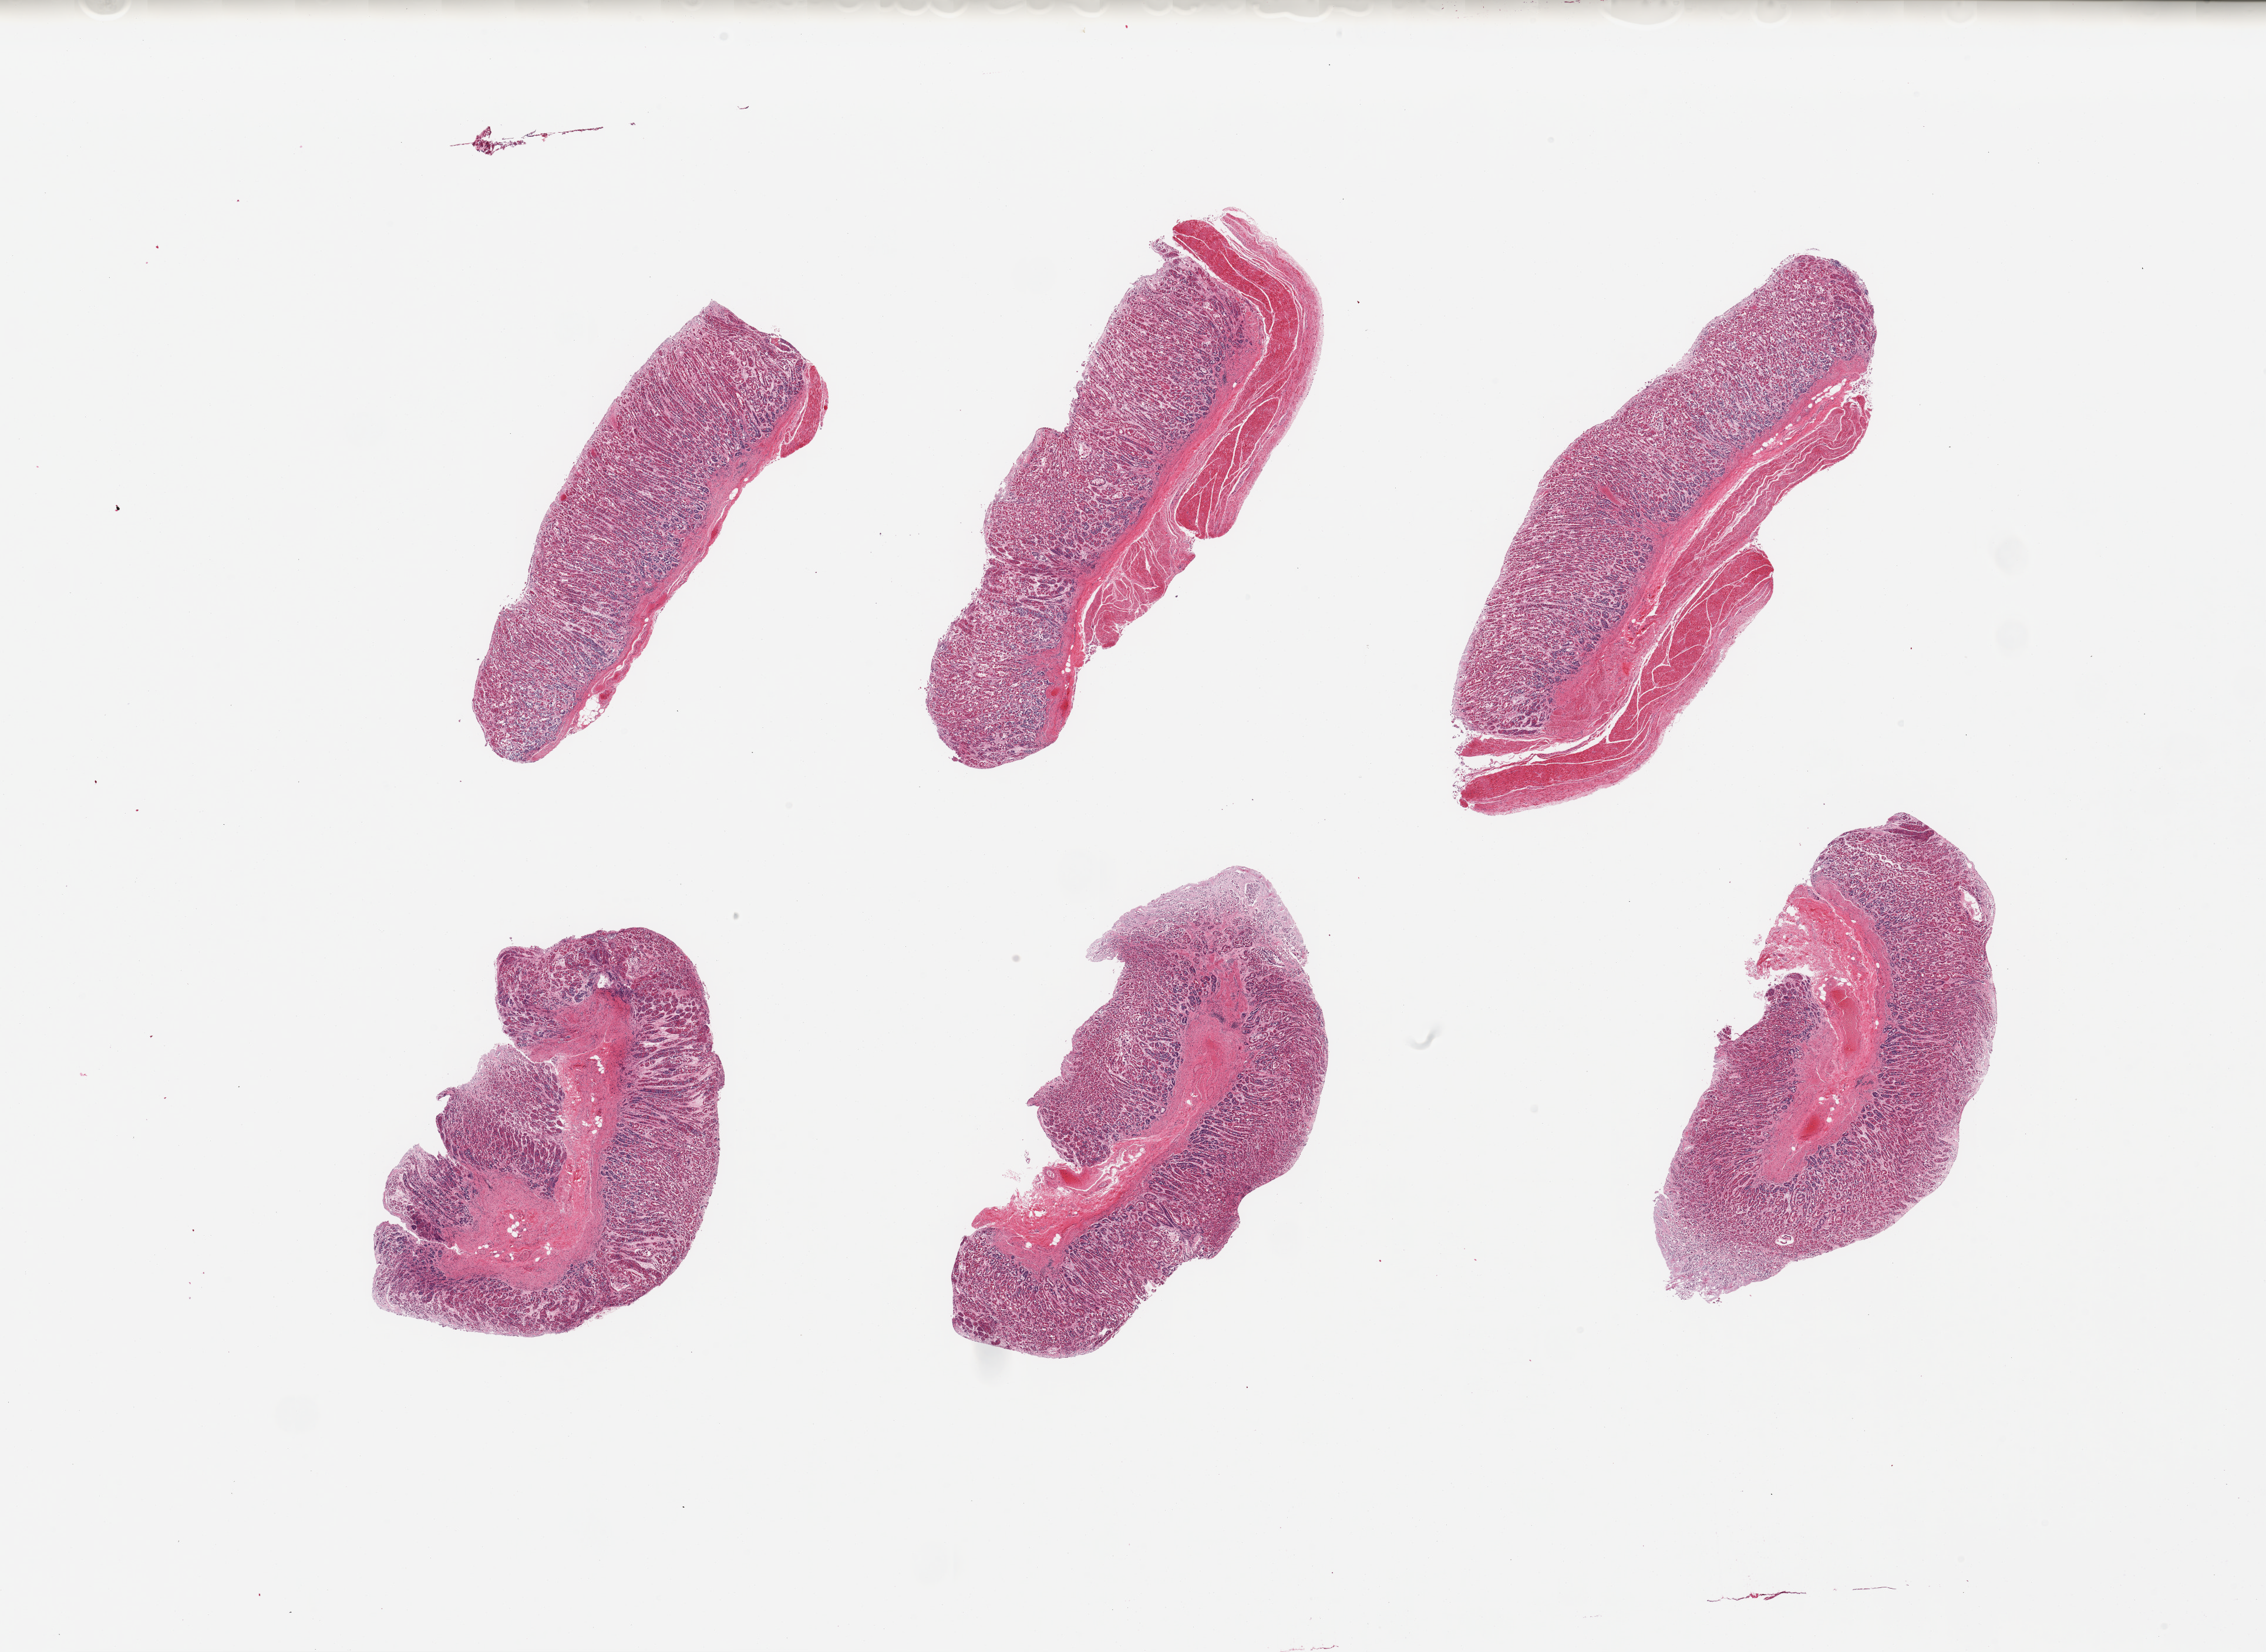
H&E whole-slide image, a low-resolution overview of the entire scanned area, about 30.5 x 22.3 mm. PAXgene-fixed, paraffin-embedded tissue. Target tissue: stomach. Tissue donor sample. Male donor.
Reviewer comment on this tissue sample: 6 pieces; 2 of 6 have full thickness, other 4 have no muscularis in sections; no lesions.